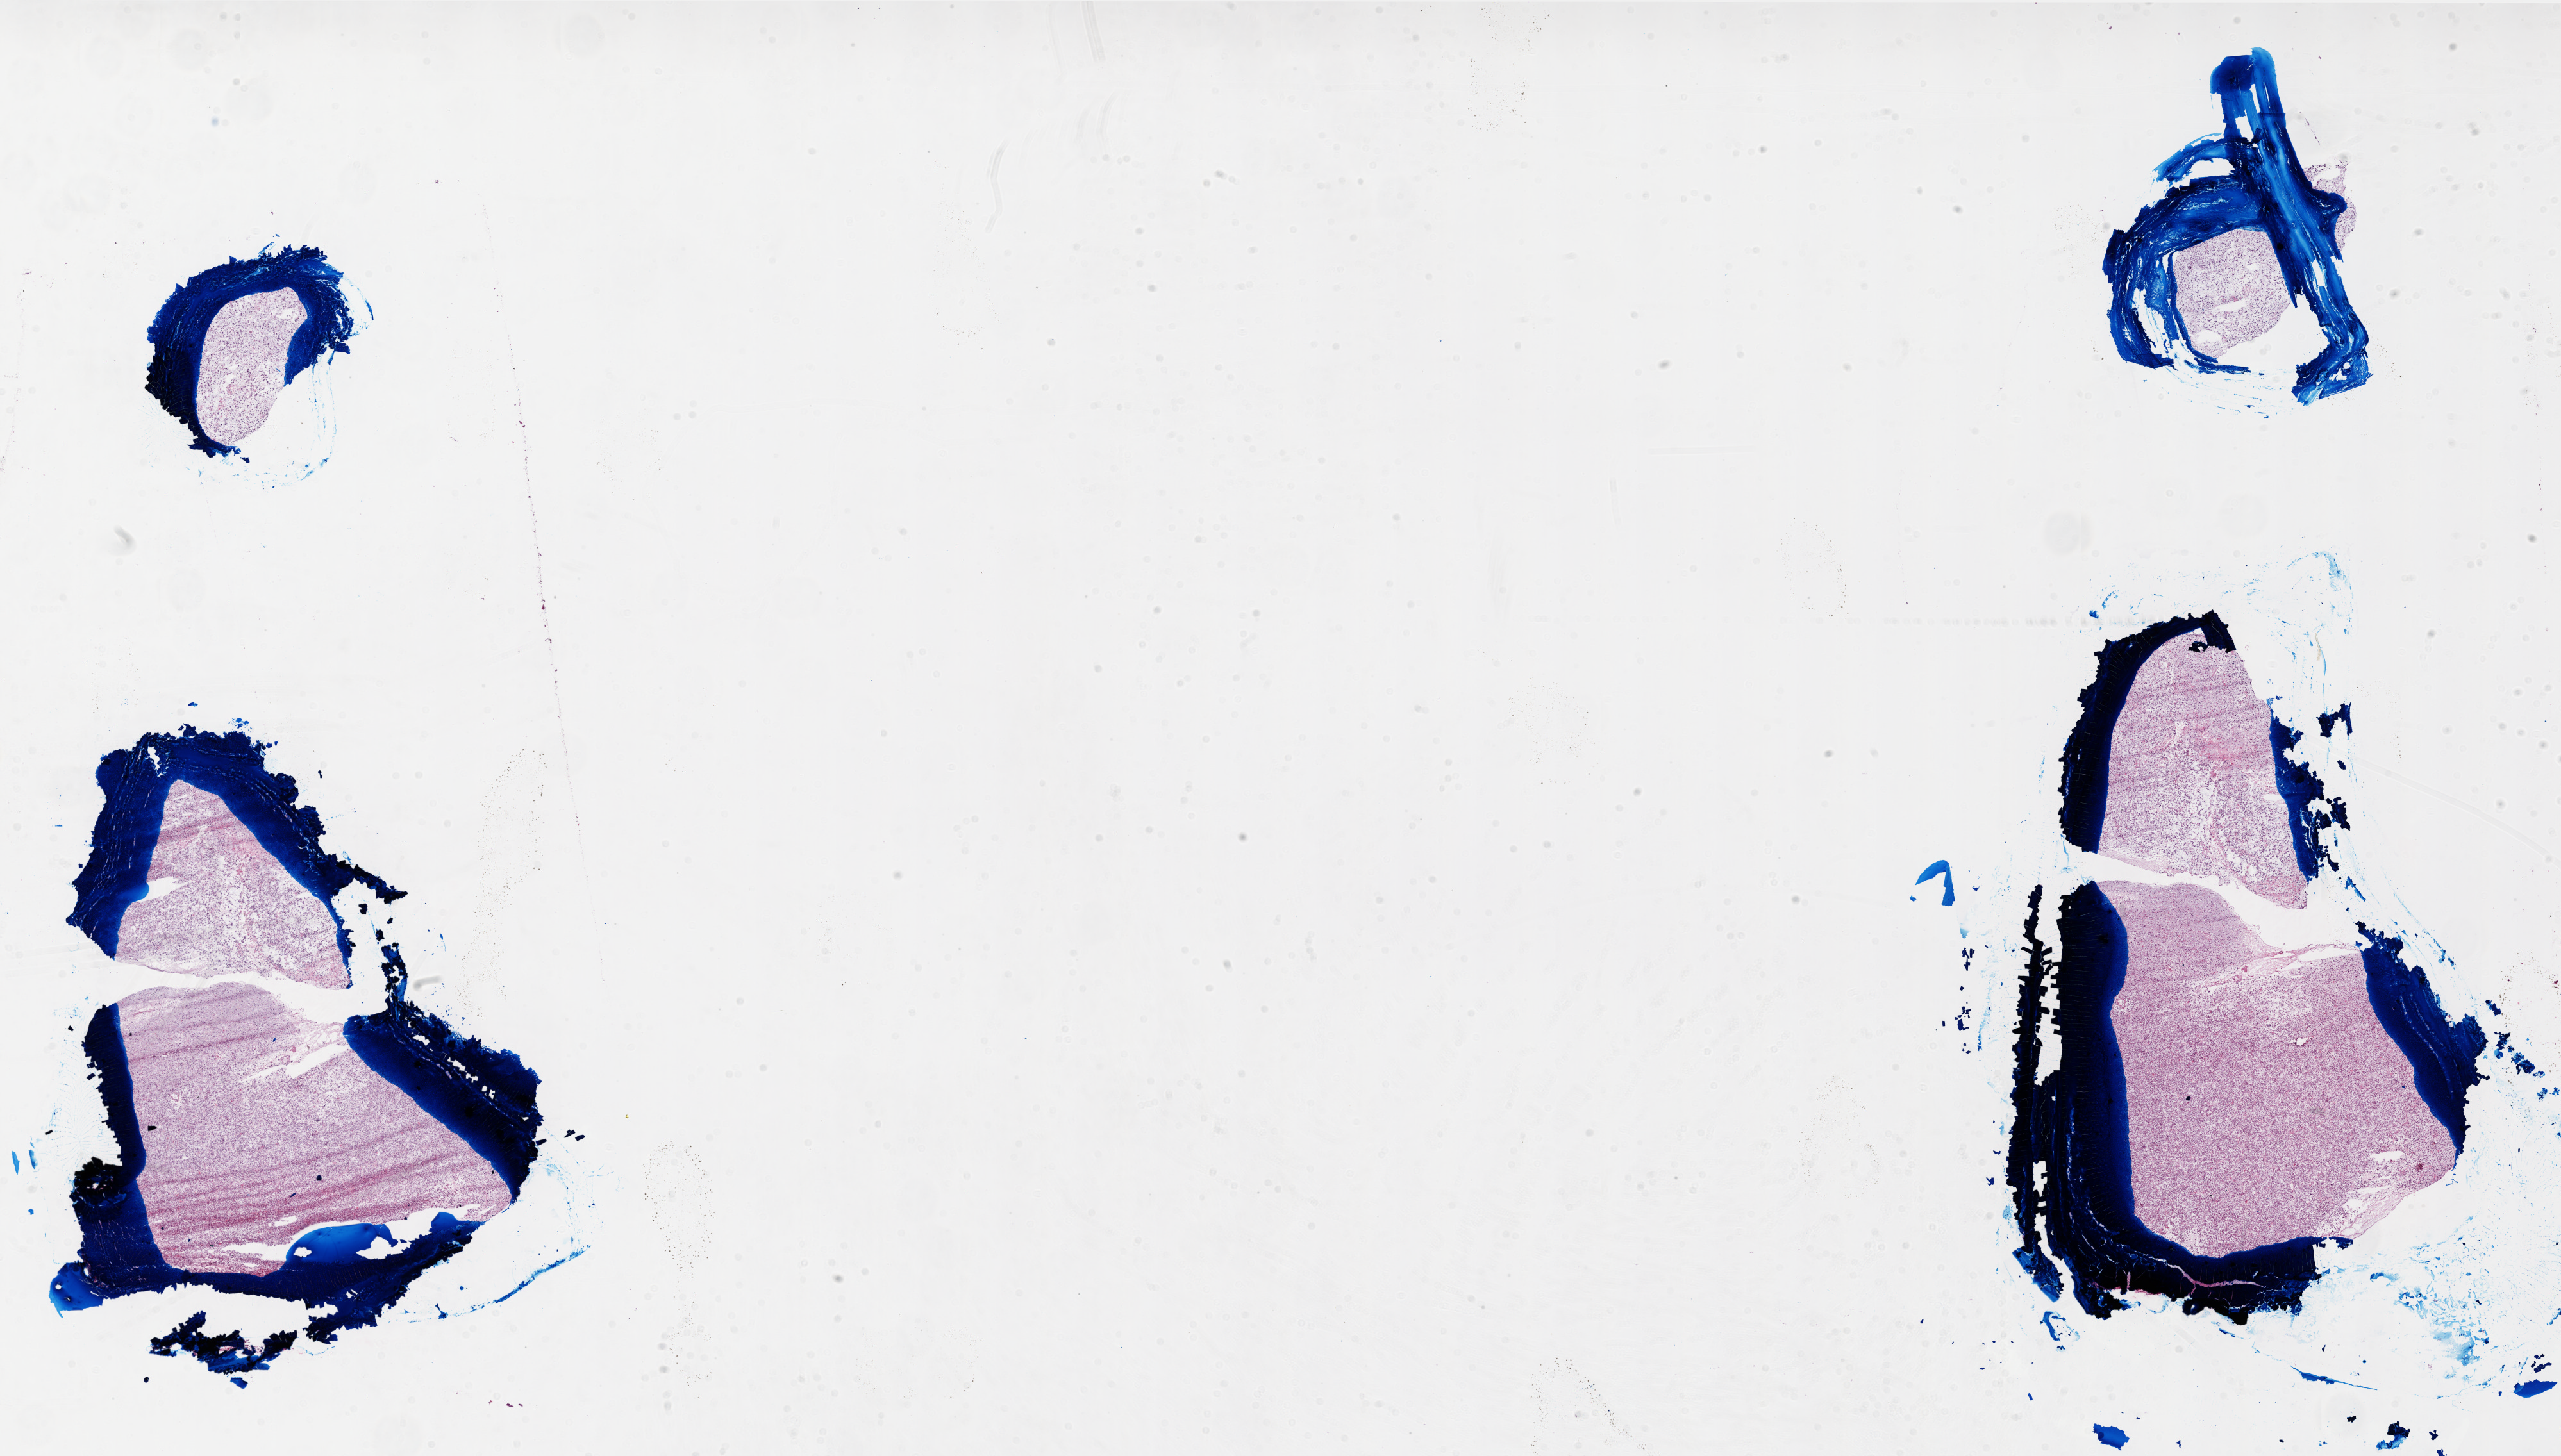
Whole-slide histology image, H&E — low-resolution overview of the scanned area, about 32.0 x 18.2 mm, frozen section from the top of the tissue portion, sample: primary tumour, brain. Male patient; age at initial diagnosis 25 years. Pathologist review of this section (percent, as recorded): tumour cells 100%, tumour nuclei 100%, normal cells 0%, stromal cells 0%, necrosis 0%.
Histologic diagnosis: Glioblastoma.